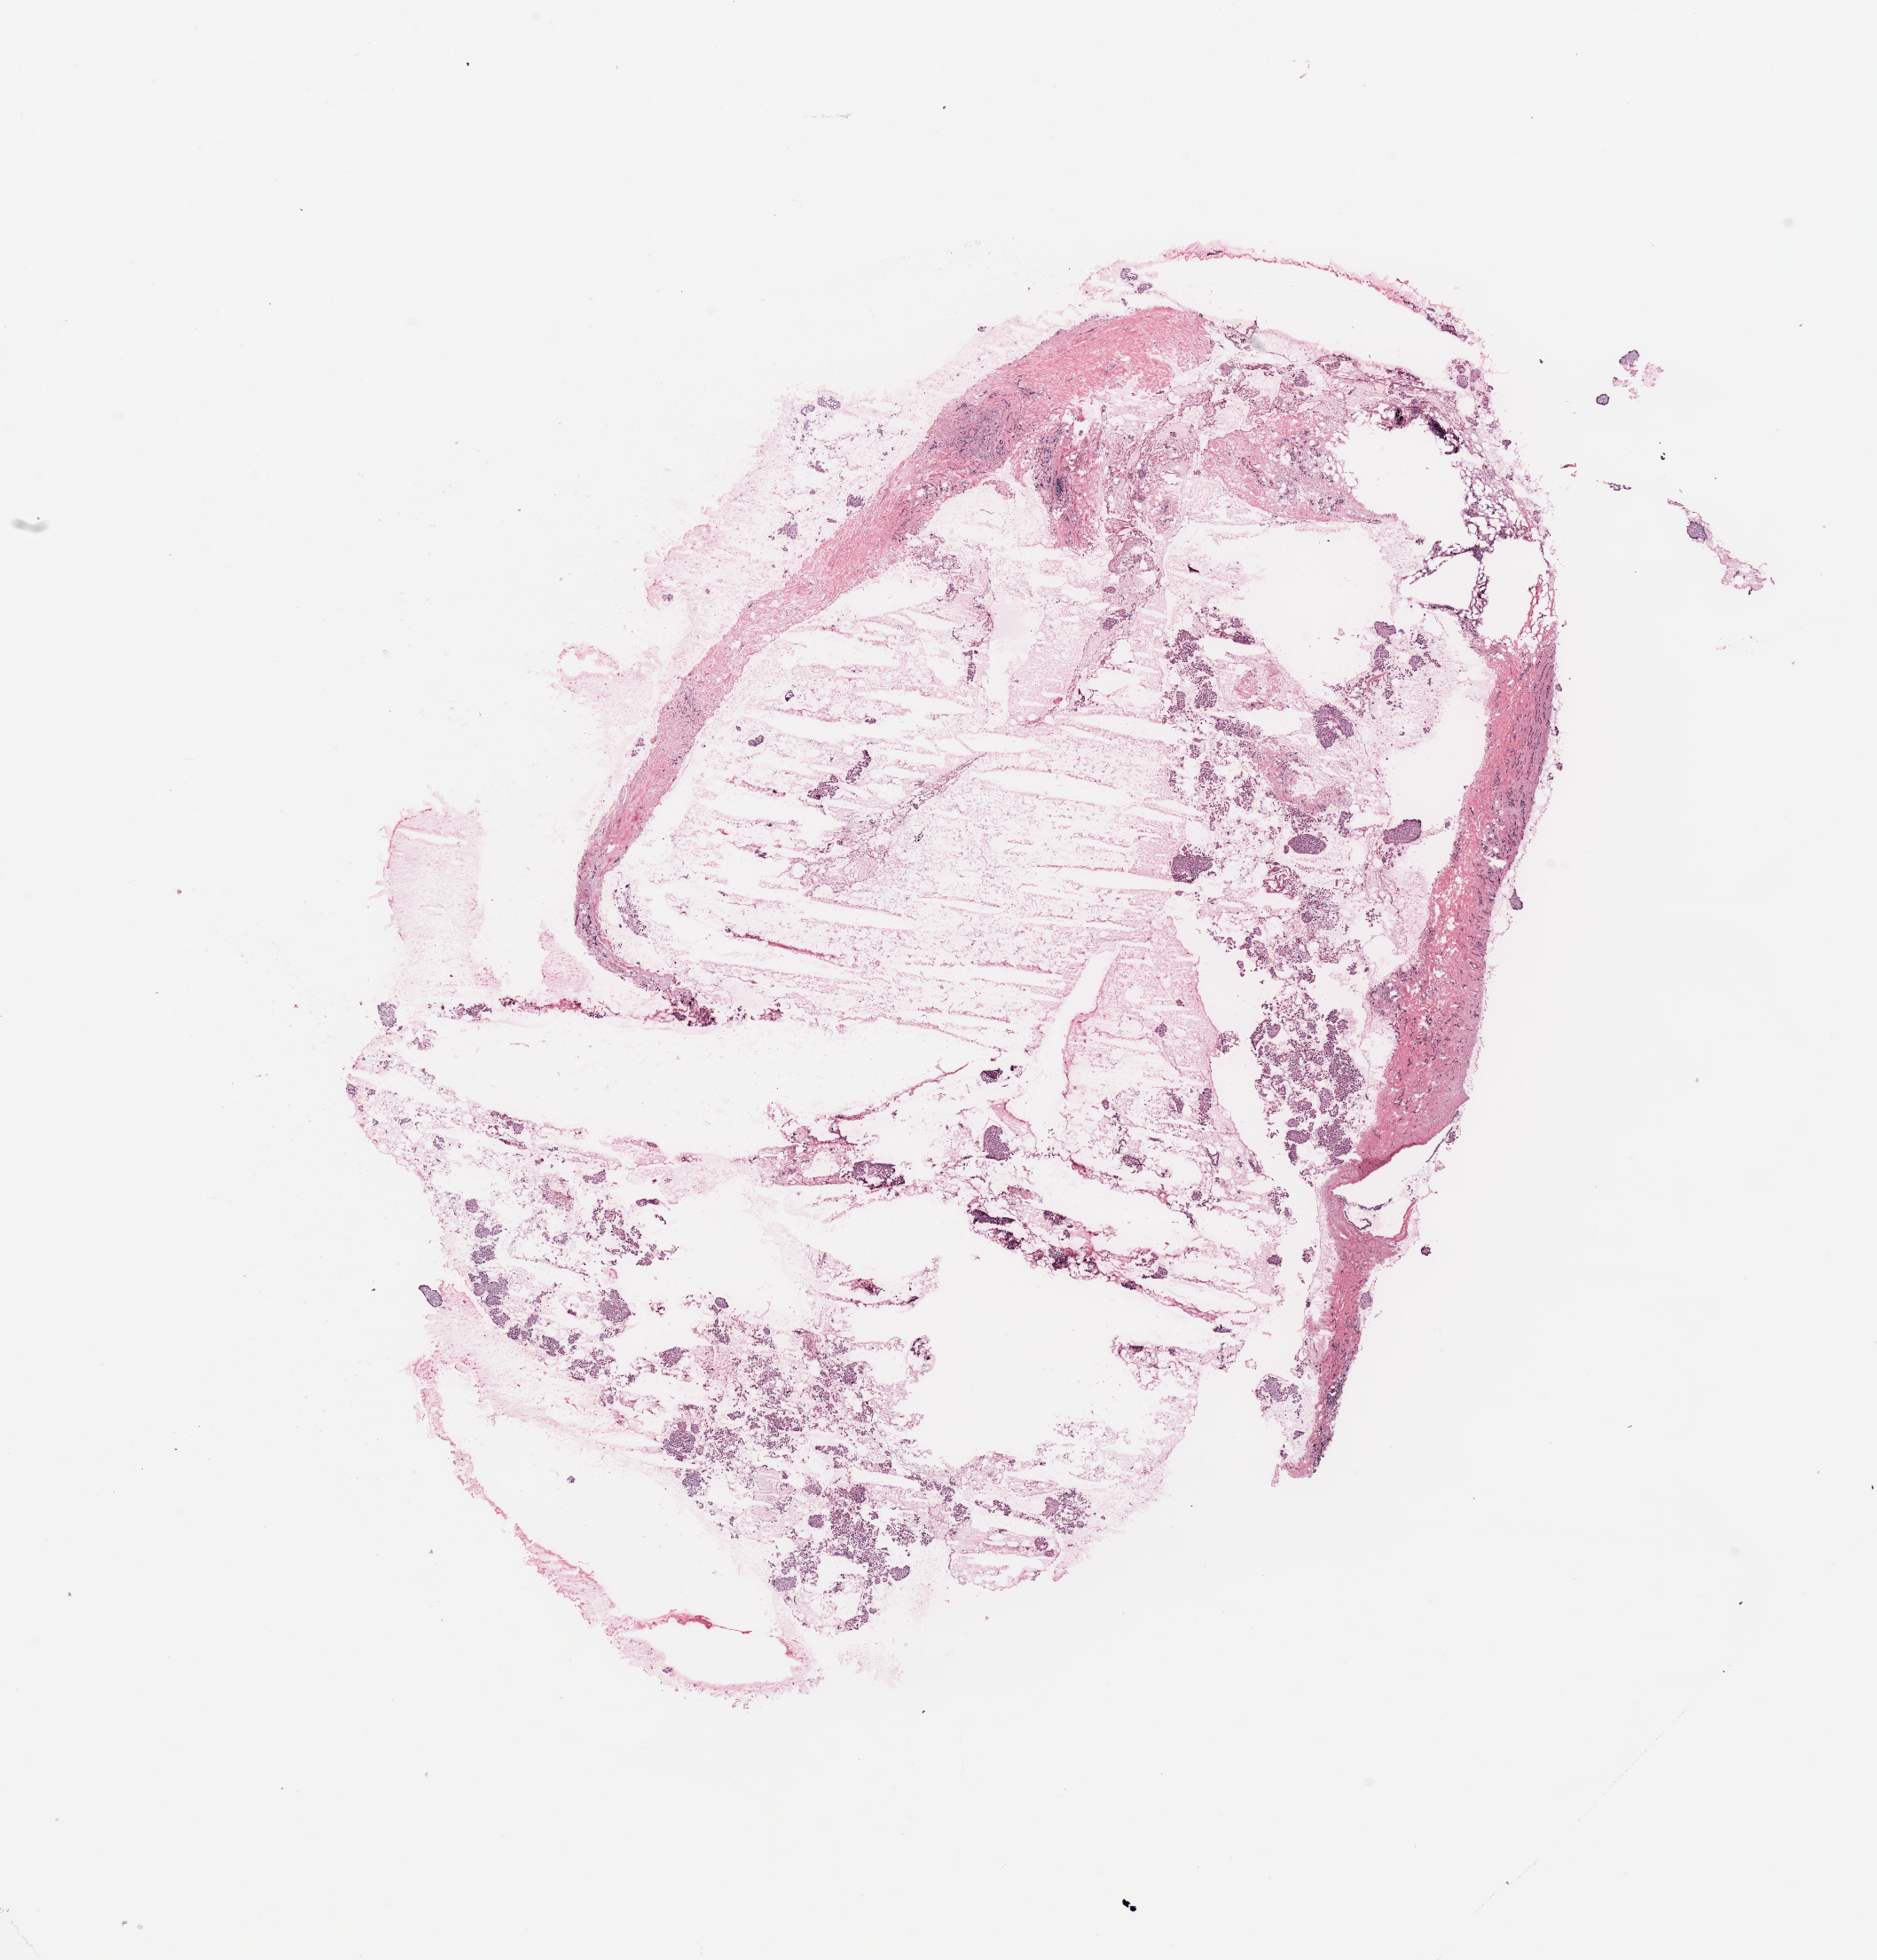
Whole-slide histology image, H&E, low-resolution overview of the scanned area, about 16.7 x 17.5 mm. Tumour tissue sample, breast. 62-year-old female patient.
Diagnosis: Infiltrating duct carcinoma, NOS. AJCC pathologic stage: IIIA.